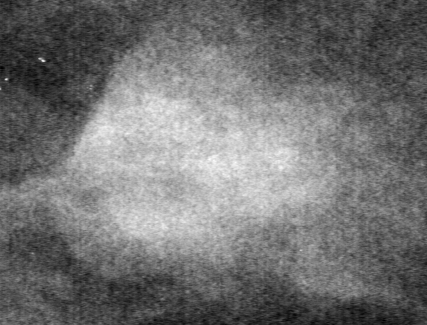
Crop from a digitized film mammogram around one marked abnormality, right breast, MLO view.
- Marked abnormality: mass, shape lobulated, margins circumscribed; BI-RADS assessment category 4; subtlety rating 4 on a 1 (subtle) to 5 (obvious) scale; pathology result (as recorded, not read from the image): benign.